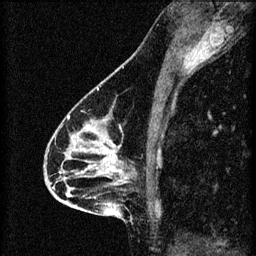
Breast MRI (dynamic contrast-enhanced), one sagittal slice; position 35 of 60 along the scan axis; 3 images stored at this slice position (order not interpretable as contrast timing); 1.5 T; TE 4.2 ms, TR 8.2 ms; 256 × 256 image matrix, field of view 180 × 180 mm. Patient: female, 46 years.
Annotated regions visible in this slice (semi-automatic segmentation, software-assisted and operator-edited):
- analysis volume of interest (the breast-tissue region the enhancement analysis was run in; not a lesion): bounding box <55,114,148,209> (left, top, right, bottom; pixels)
- tumour enhancement mask (voxels above the 70 % enhancement threshold inside the analysis volume of interest): <66,116,122,195>